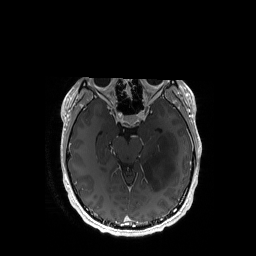
Brain MRI from a brain-tumour surgery series, one axial slice. Slice 106 of 192 in the series (ordered by position). T1-weighted post-contrast. 1 mm slice thickness. 256 × 256 image matrix. Case-level facts recorded for this patient, not image findings: histopathology: Astrocytoma; WHO grade: 3; IDH mutation: yes.
Structures marked on this image (expert manual segmentation):
- tumour: bounding box <142,131,178,192> (left, top, right, bottom; pixels)